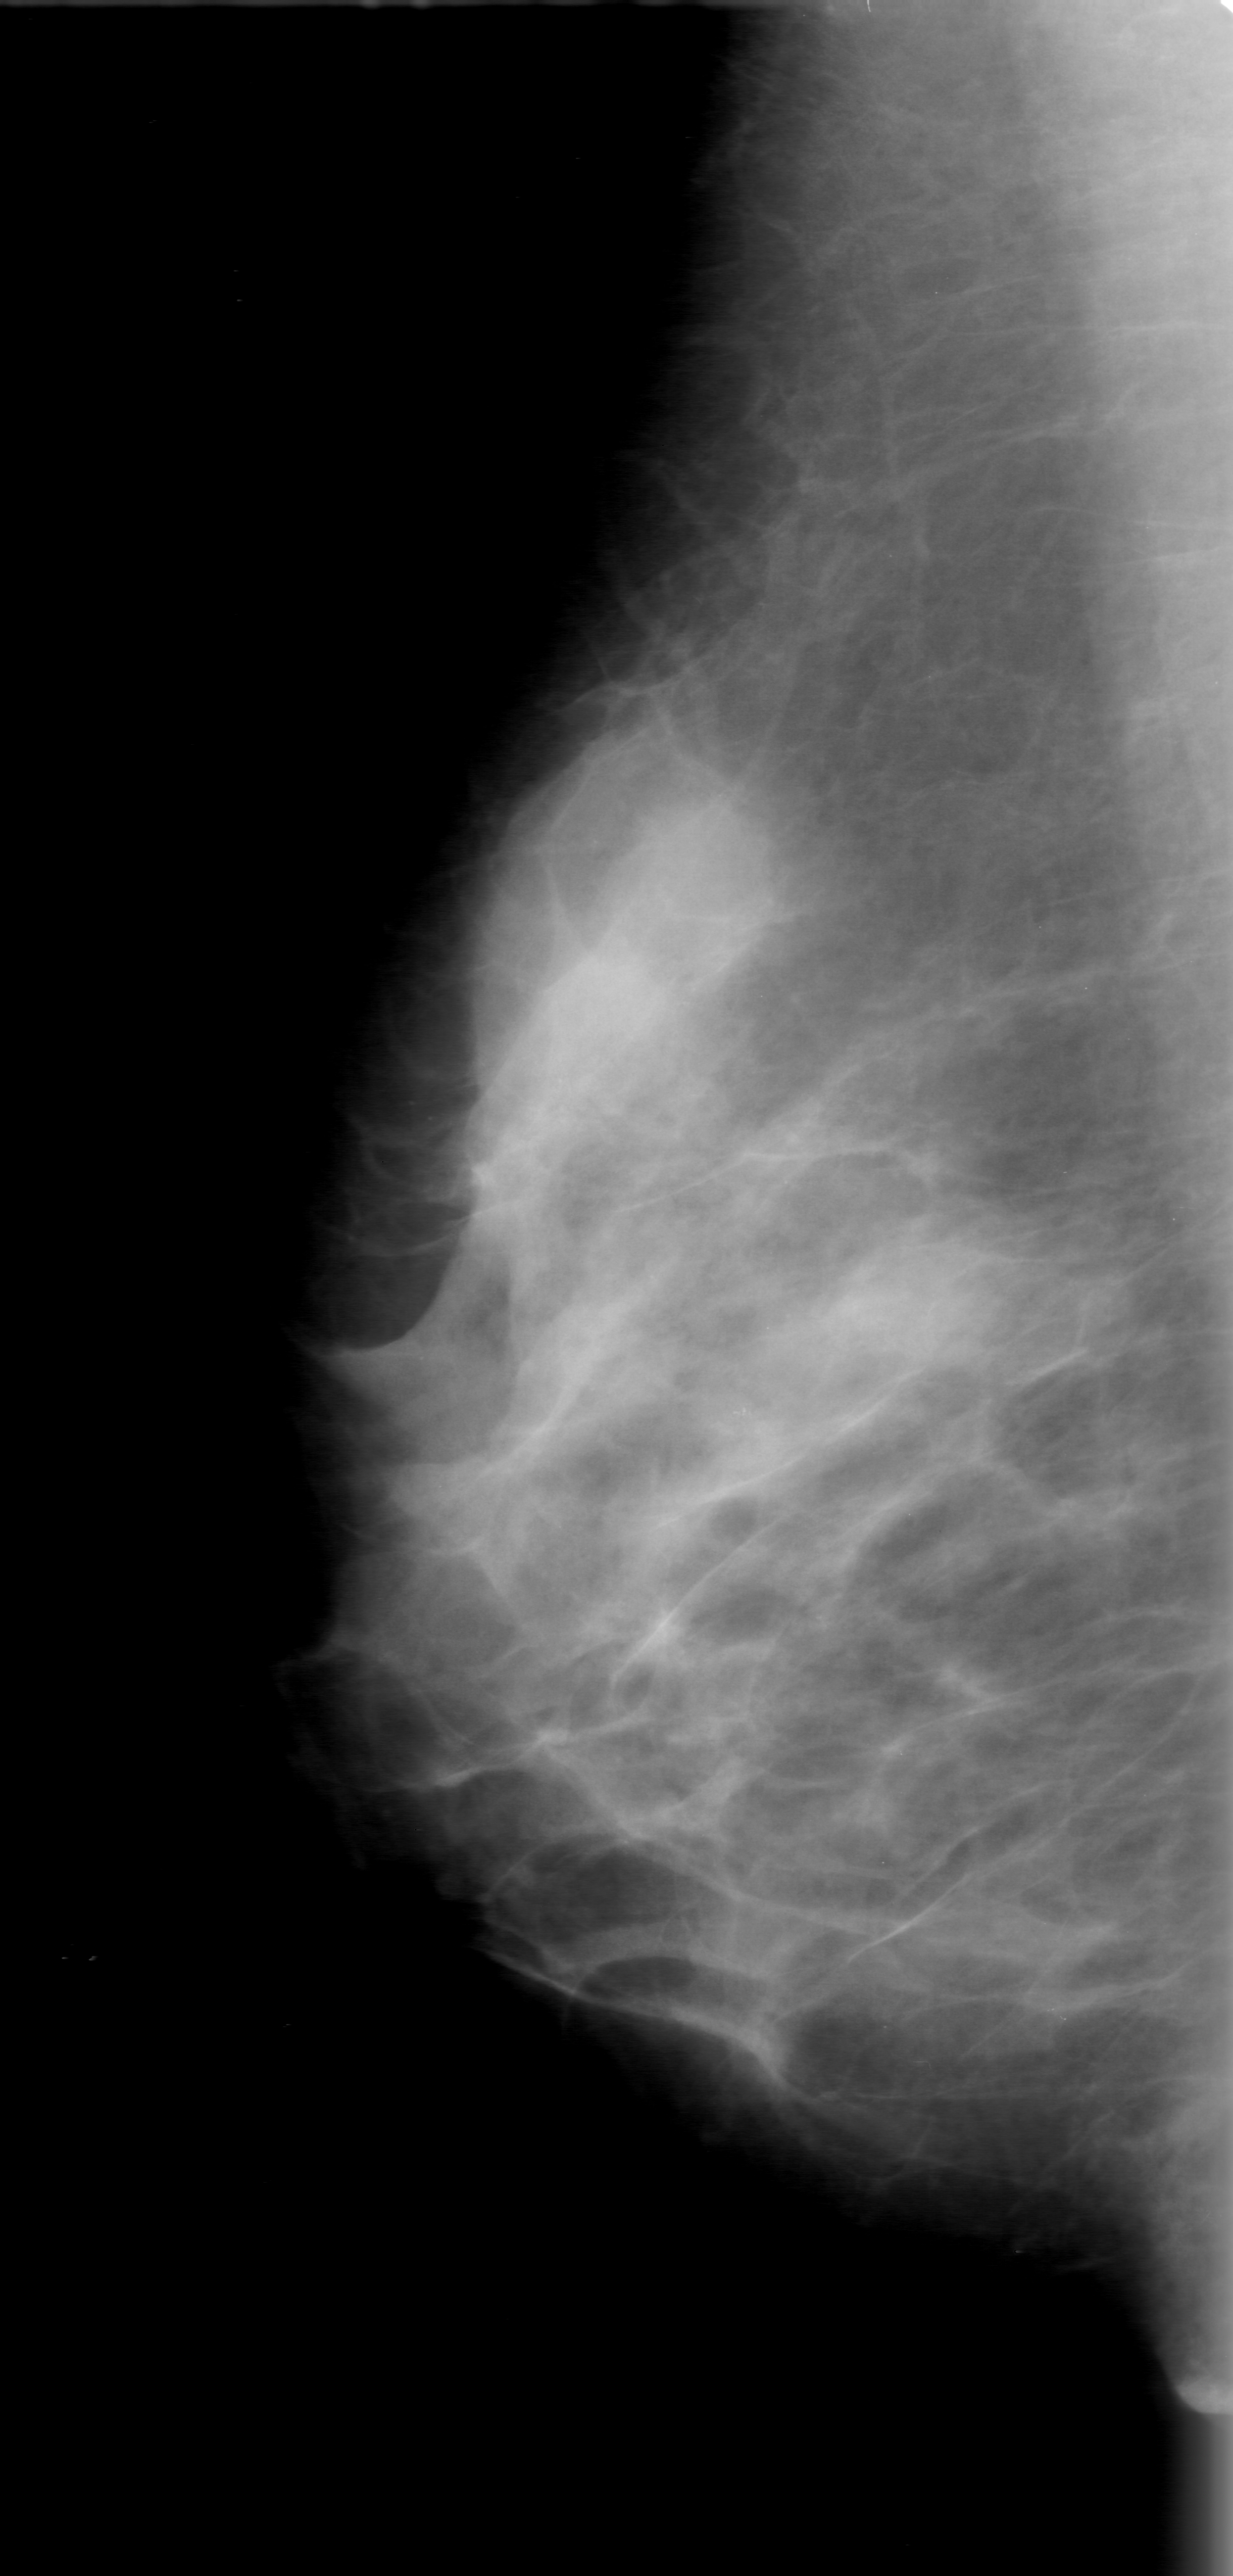
Scanned film-screen mammogram; right breast; MLO view; BI-RADS breast density category 3 (scale 1–4).
Abnormality record for this image: calcifications, morphology amorphous, distribution segmental; BI-RADS assessment category 0 (incomplete: needs additional imaging); subtlety rating 3 on a 1 (subtle) to 5 (obvious) scale; pathology result (as recorded, not read from the image): benign.